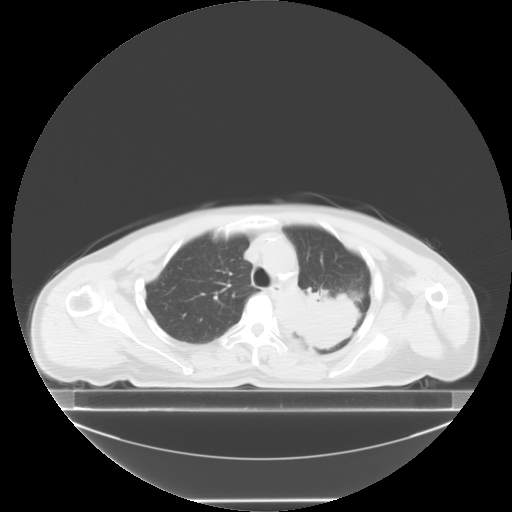
Chest CT, one axial slice. Slice 9 of 24 in the series (ordered by position). 120 kVp. Lung window (W 1500 / L -600 HU). 5 mm slice thickness. 512 × 512 image matrix, field of view 500 × 500 mm. Patient: female, 74 years. Case-level facts recorded for this patient, not image findings: clinical TNM (as recorded): T3 N1 M1c; histopathological grade: G3.
Annotated regions visible in this slice (bounding box drawn by a radiologist):
- lung tumour (recorded histology: small cell carcinoma): box from (x=295, y=285) to (x=355, y=353) px